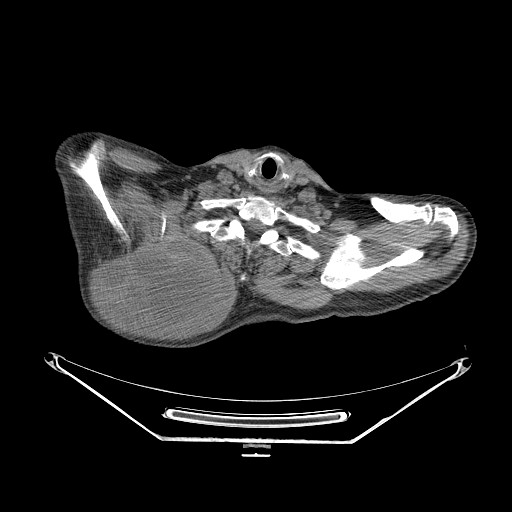
CT of an extremity soft-tissue mass (from a PET/CT study), one axial slice; slice 209 of 267 in the series (ordered by position); reconstruction kernel STANDARD; soft-tissue window (W 400 / L 40 HU); 3.75 mm slice thickness; 512 × 512 image matrix, field of view 500 × 500 mm. Male patient. From the clinical record (not read from this slice): histological type: pleiomorphic spindle cell undifferentiated; grade: high; site of the primary tumour: right parascapusular.
Outlined on this slice (expert contour drawn on MRI and transferred to this co-registered scan by the dataset authors):
- gross tumour volume including surrounding oedema: box from (x=93, y=235) to (x=232, y=327) px
- gross tumour volume (mass): (x=96, y=237)–(x=222, y=323)